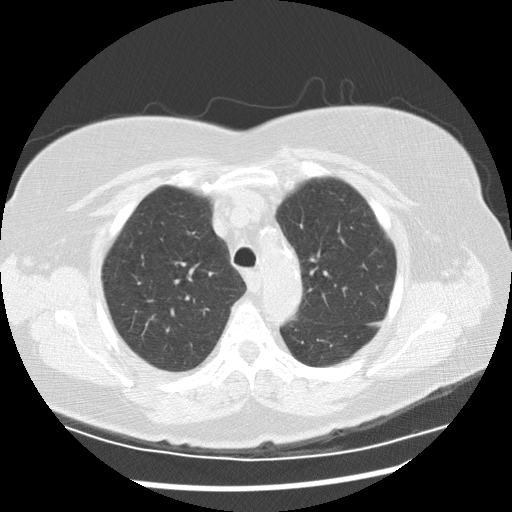
Chest CT (low-dose screening protocol), one axial image, second screening round (one year after baseline), lung window (W 1500 / L -600 HU), 2.5 mm slice thickness. Female, age 72 years at enrolment. Current smoker at enrolment.
Lesion marked by an expert reader, bounding box <143,309,166,331> (left, top, right, bottom; pixels). Screening reader's record for this exam: no non-calcified nodule ≥4 mm recorded. Lung cancer was diagnosed 507 days after this screen (after the third annual screen): squamous cell carcinoma, NOS, right upper lobe, poorly differentiated (G3), stage IIIA (AJCC 6th edition), 22 mm at pathology.